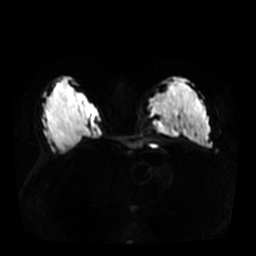
Breast MRI, one axial slice. Position 19 of 36 along the scan axis. Diffusion-weighted series; image 2 of 4 stored at this slice position (different b-values; order by instance number). 3 T. 5 mm slice thickness. 256 × 256 image matrix, field of view 340 × 340 mm. Female patient.
Outlined on this slice (outlined manually by an expert reader):
- tumour on diffusion-weighted imaging: bounding box <152,93,178,137> (left, top, right, bottom; pixels)